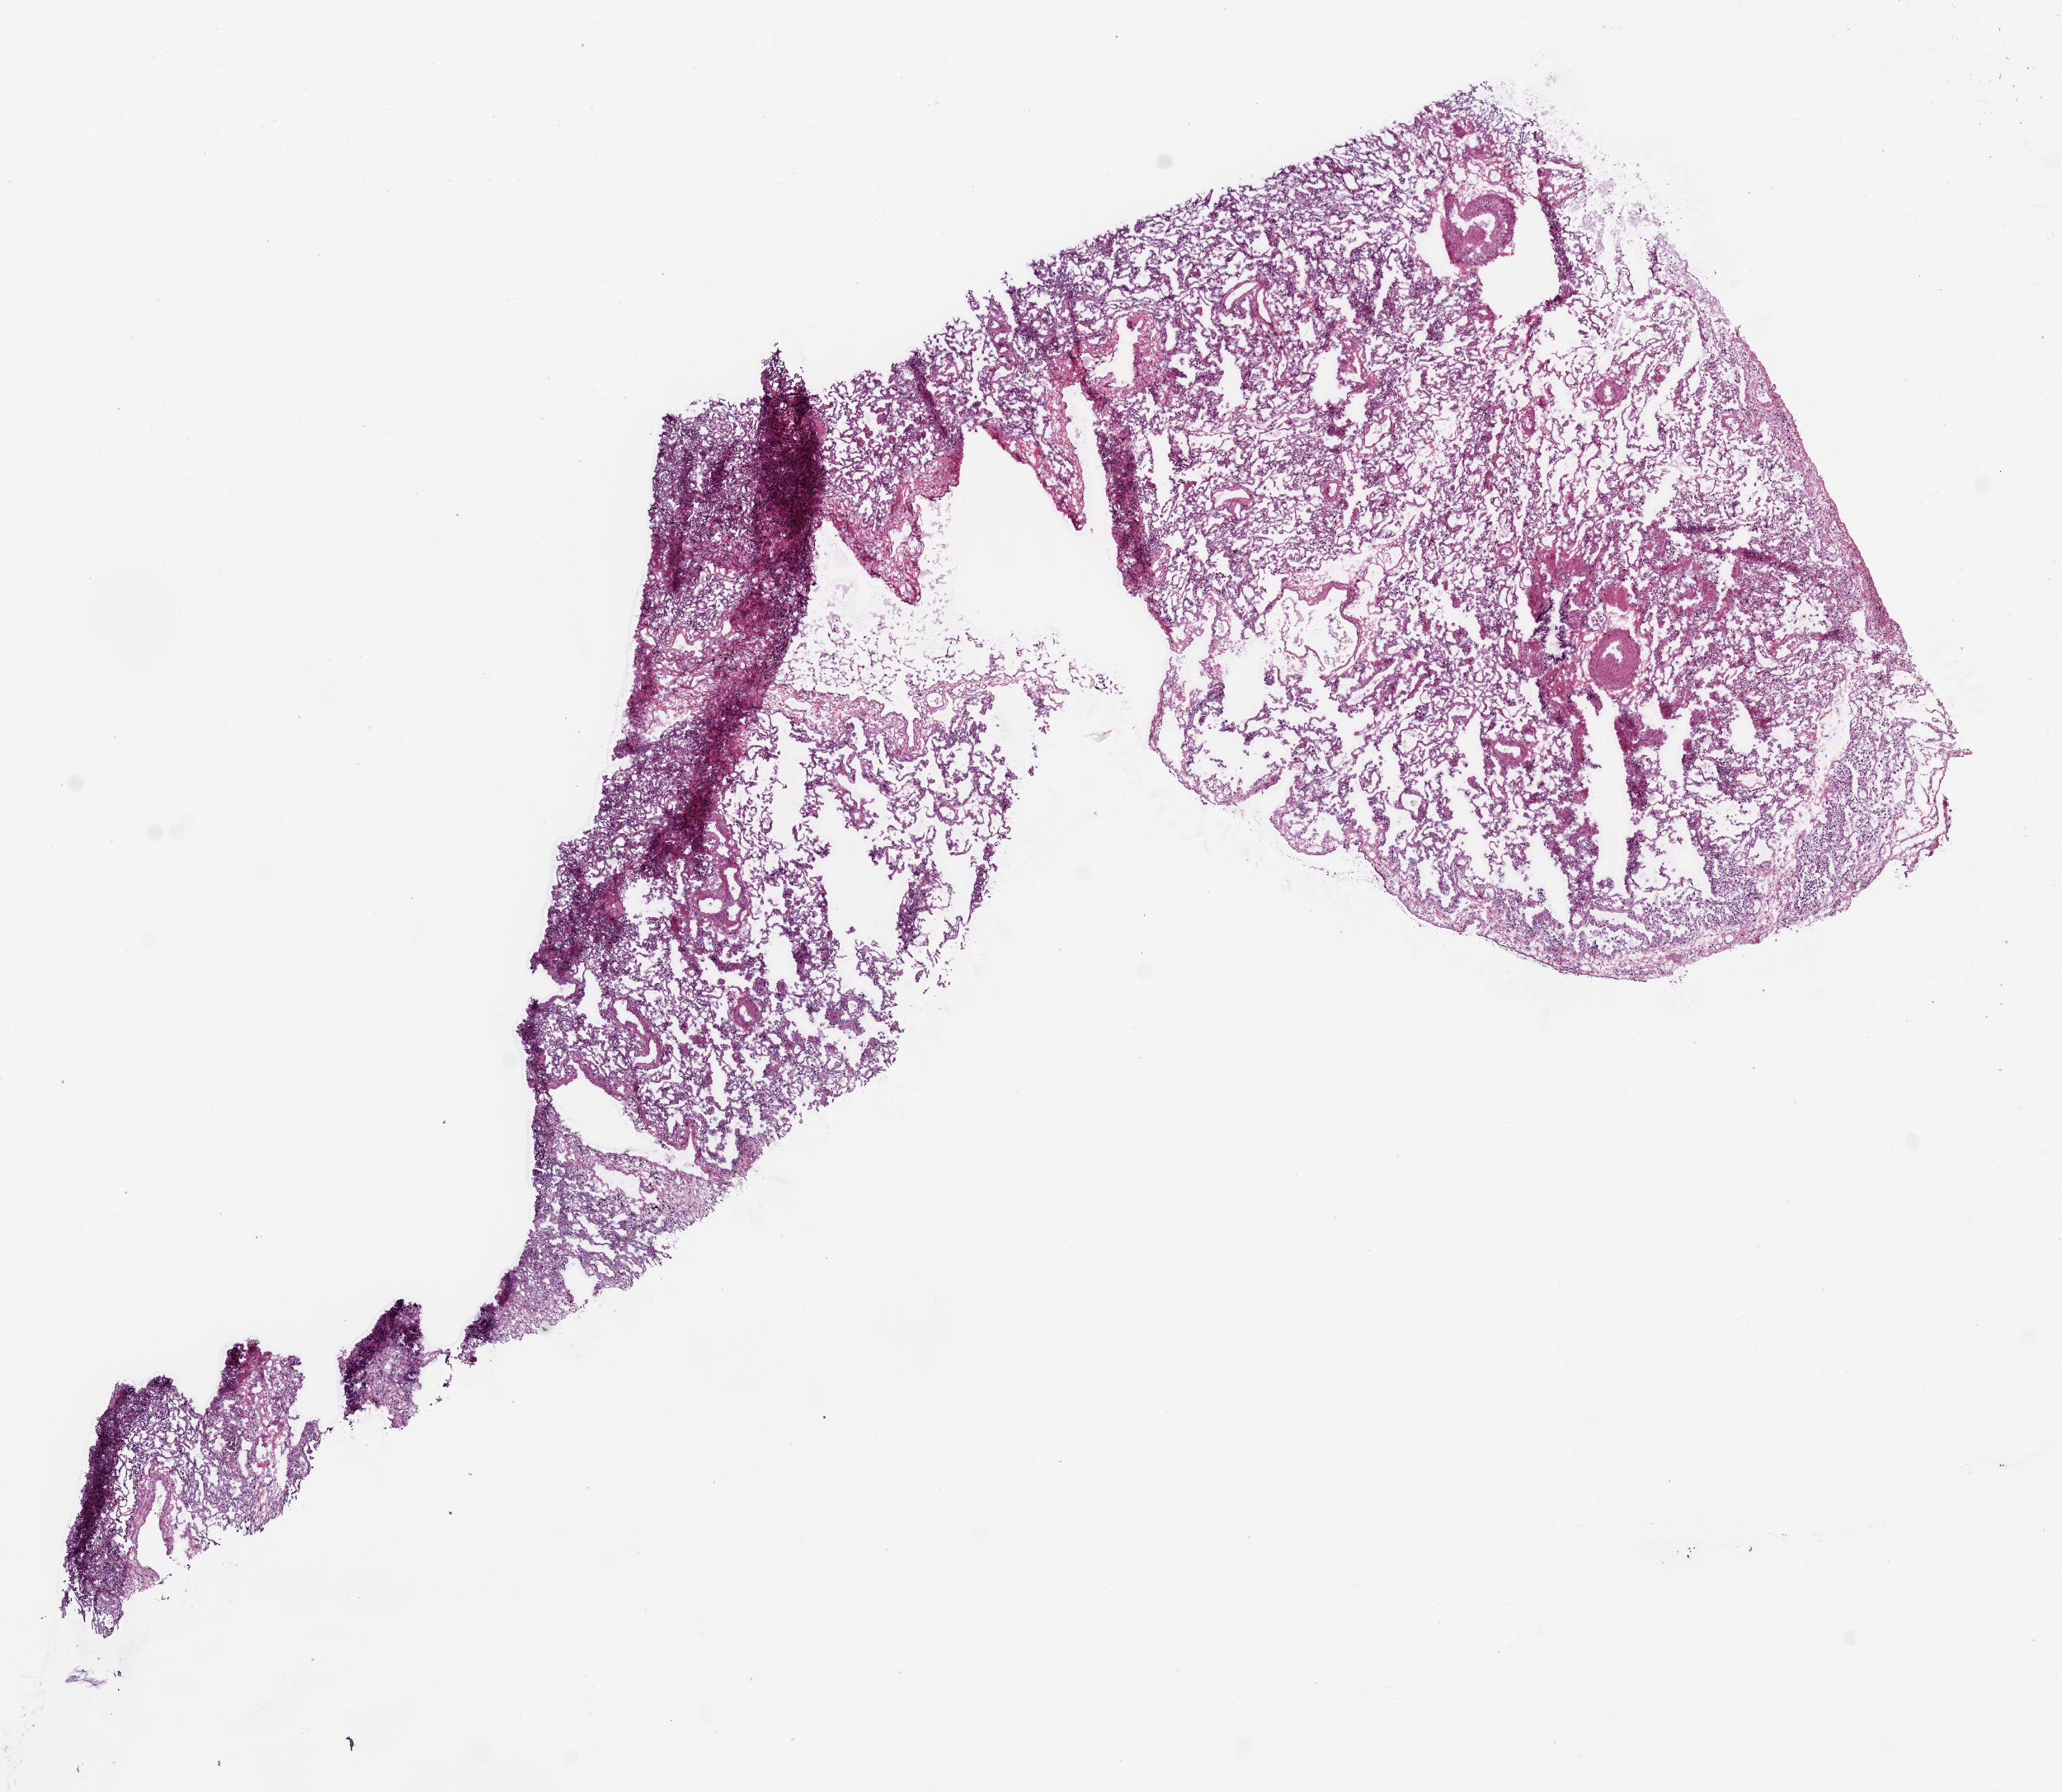
Digitized Hematoxylin and eosin (H&E) stained tissue section (whole slide), a low-resolution overview of the entire scanned area, about 10.0 x 8.7 mm. Frozen section. Sample: solid tissue normal (non-tumour tissue), lung. Female, age 62 years at initial diagnosis.
This section: solid tissue normal sample (biorepository sample class). Patient diagnosis: Squamous cell carcinoma, NOS.